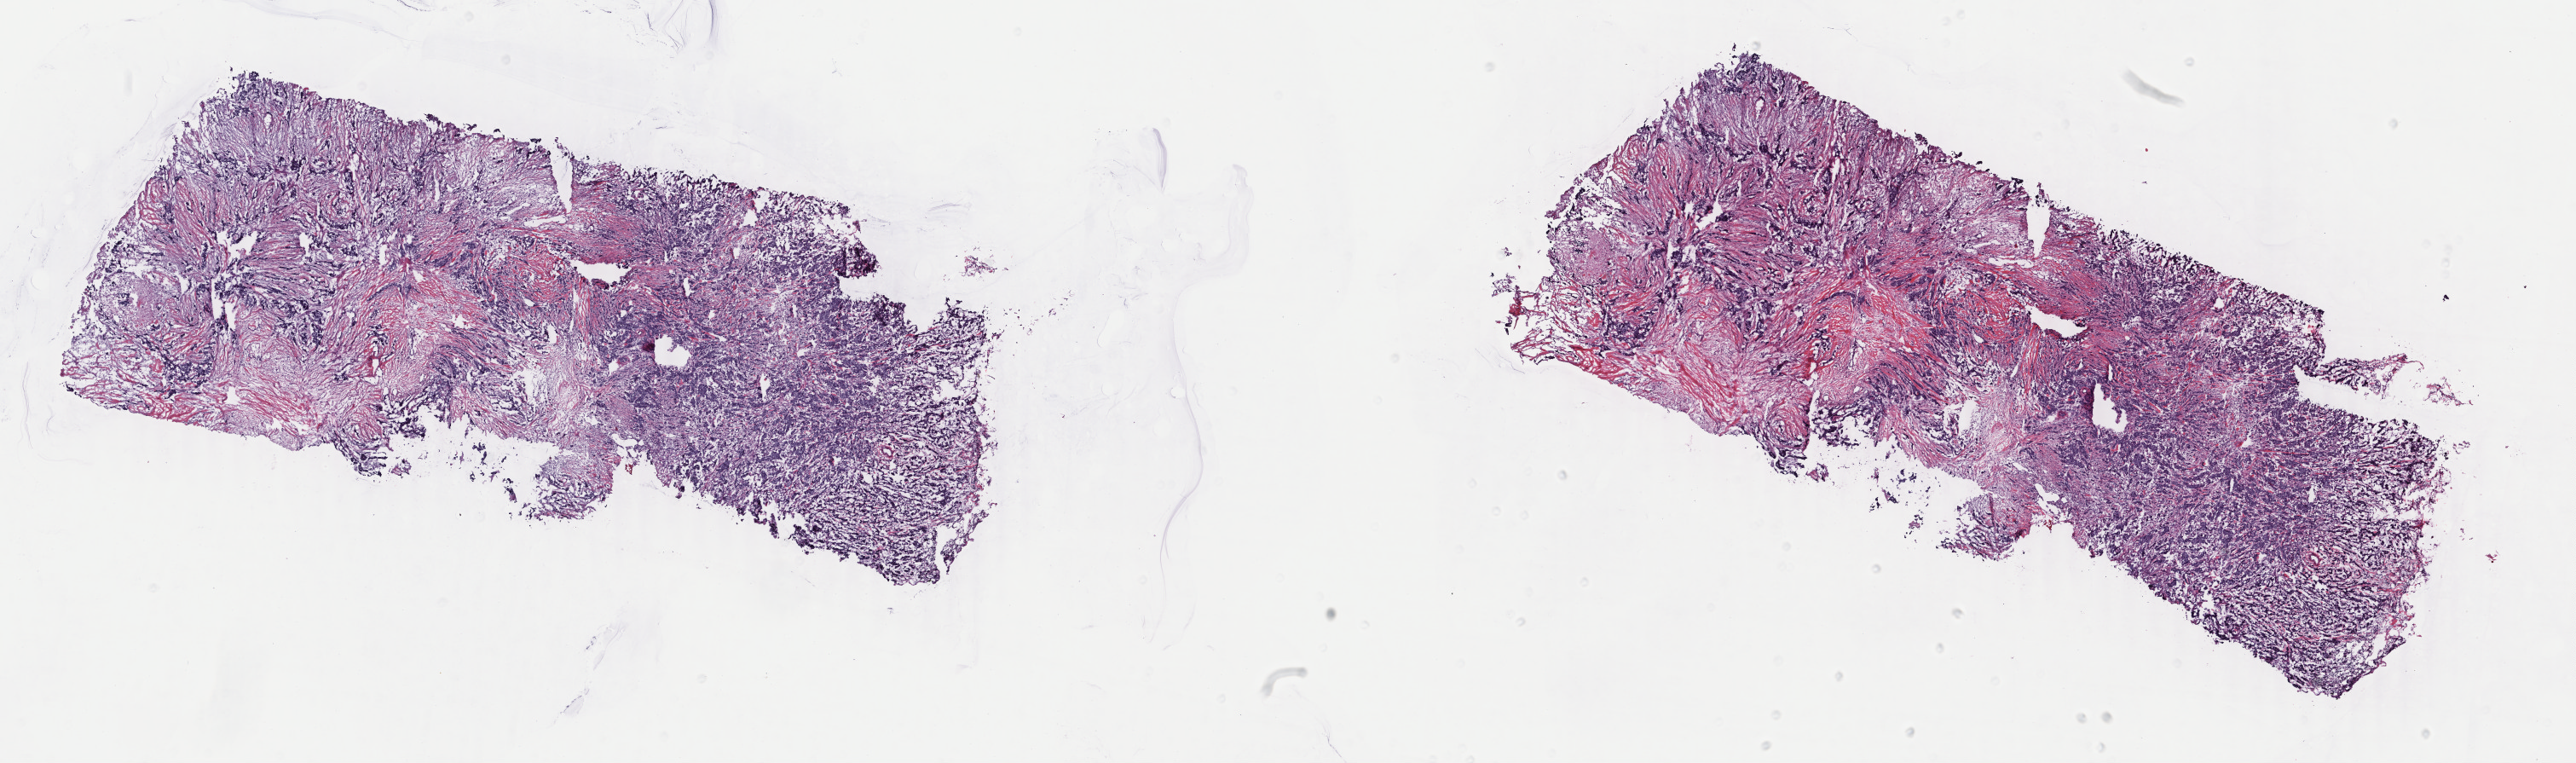
Whole-slide histology image, Hematoxylin and eosin (H&E) stained, a low-resolution overview of the entire scanned area, about 24.0 x 7.1 mm (from a 40x scan); frozen section from the top of the tissue portion; primary tumour sample from the breast. Female, age 55 years at initial diagnosis. Slide review estimates, as recorded: tumour cells 100%, tumour nuclei 80%, normal cells 0%, stromal cells 0%, necrosis 0%. Inflammatory infiltration, as recorded: lymphocyte infiltration 0%, monocyte infiltration 0%, neutrophil infiltration 0%.
AJCC pathologic stage: IA (7th edition). Pathologic diagnosis: Infiltrating duct carcinoma, NOS.